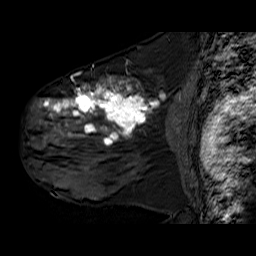
Breast MRI (dynamic contrast-enhanced), one sagittal slice; slice 38 of 60 in the series (ordered by position); dynamic contrast-enhanced series, time point 2 of 6 at this slice position (early post-contrast); 1.5 T; TE 6.3 ms, TR 32.9 ms; 4 mm slice thickness; 256 × 256 image matrix, field of view 200 × 200 mm. Female patient. From the clinical record (not read from this slice): setting: breast cancer imaged before/during neoadjuvant chemotherapy; receptor status: HER2-positive.
Annotated regions visible in this slice (semi-automatic segmentation, software-assisted and operator-edited):
- analysis volume of interest (the breast-tissue region the enhancement analysis was run in; not a lesion): bounding box [x1, y1, x2, y2] px = [30, 78, 176, 180]
- tumour enhancement mask (voxels above the 100 % enhancement threshold inside the analysis volume of interest): [43, 78, 158, 145]